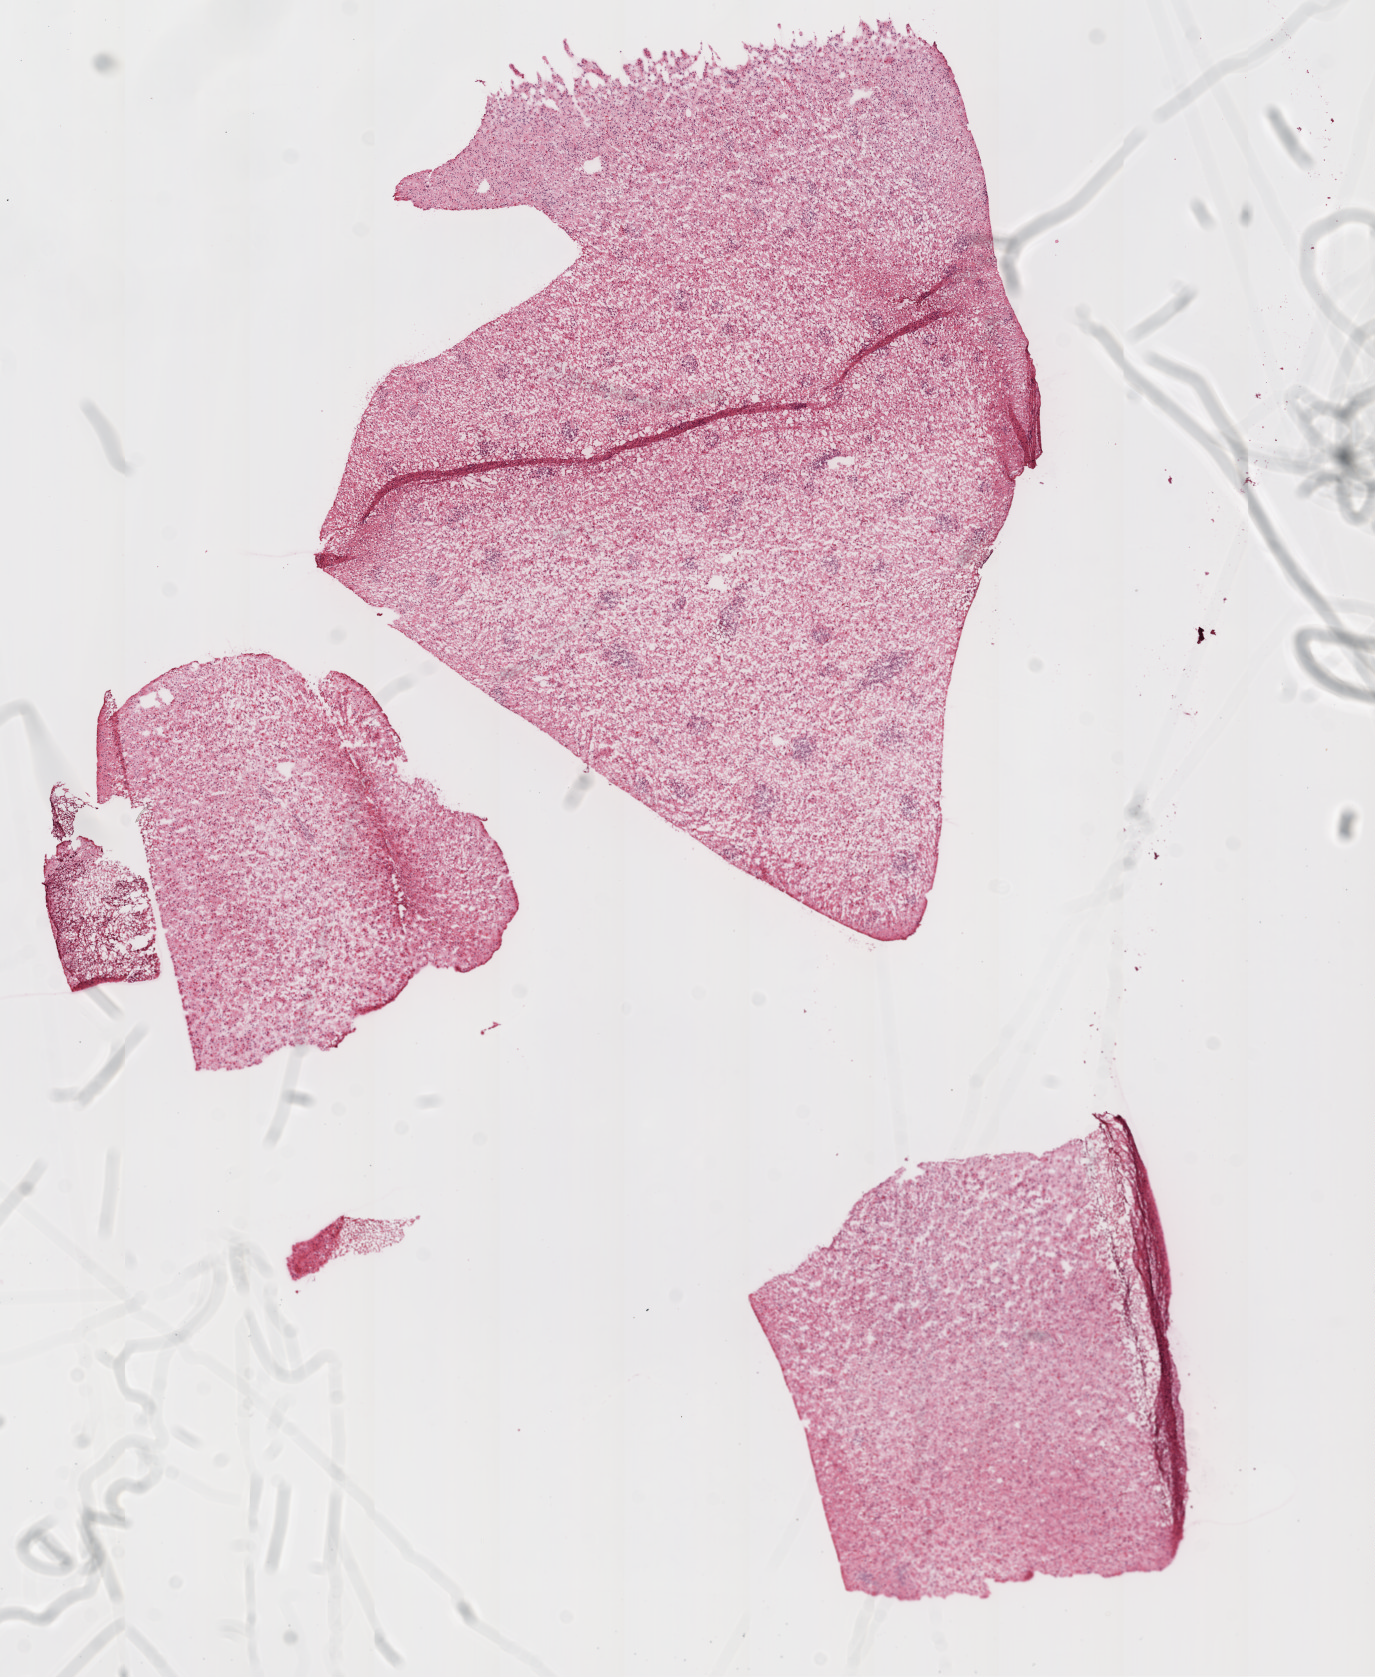
Whole-slide histology image, H&E, low-resolution overview of the scanned area, about 11.0 x 13.5 mm (from a 20x scan); frozen section from the top of the tissue portion; brain, primary tumour sample. Male patient; age at initial diagnosis 41 years. Histologic grade: G3 (poorly differentiated). Composition of this section per pathologist review: tumour cells 100%, tumour nuclei 65%, normal cells 0%, stromal cells 0%, necrosis 0%.
Histologic diagnosis: Astrocytoma, anaplastic.